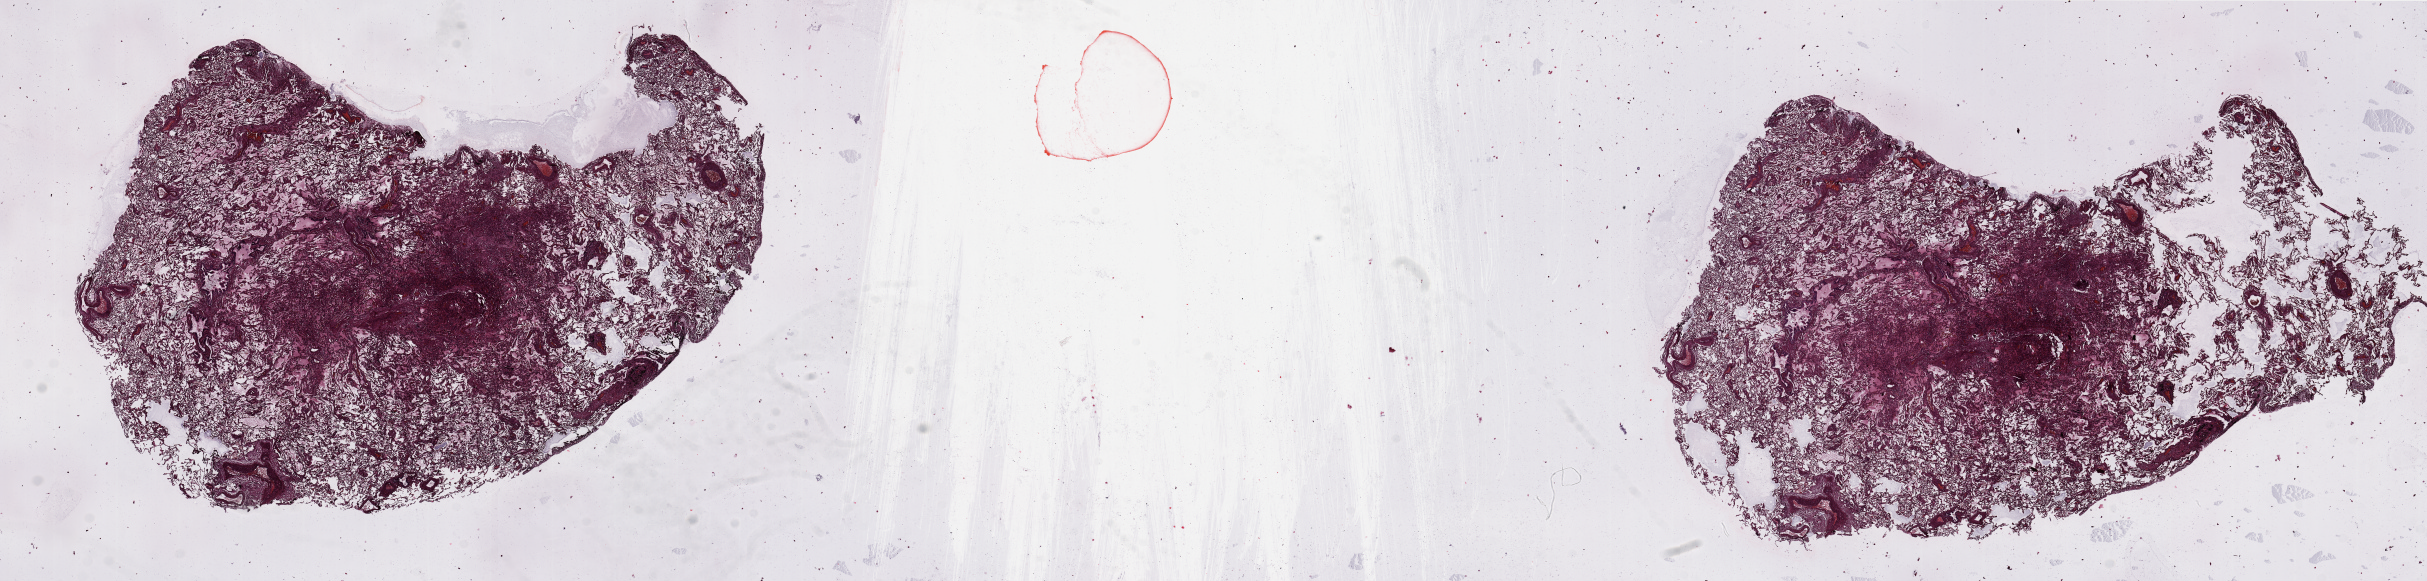
Whole-slide histology image, Hematoxylin and eosin (H&E) stained — a low-resolution overview of the entire scanned area, about 38.4 x 9.2 mm (slide scanned at 20x); normal (non-tumour) tissue sample, sampled site: lung. 66-year-old male patient.
This section: normal (non-tumour) tissue from the same patient. Patient diagnosis: Squamous cell carcinoma, NOS.